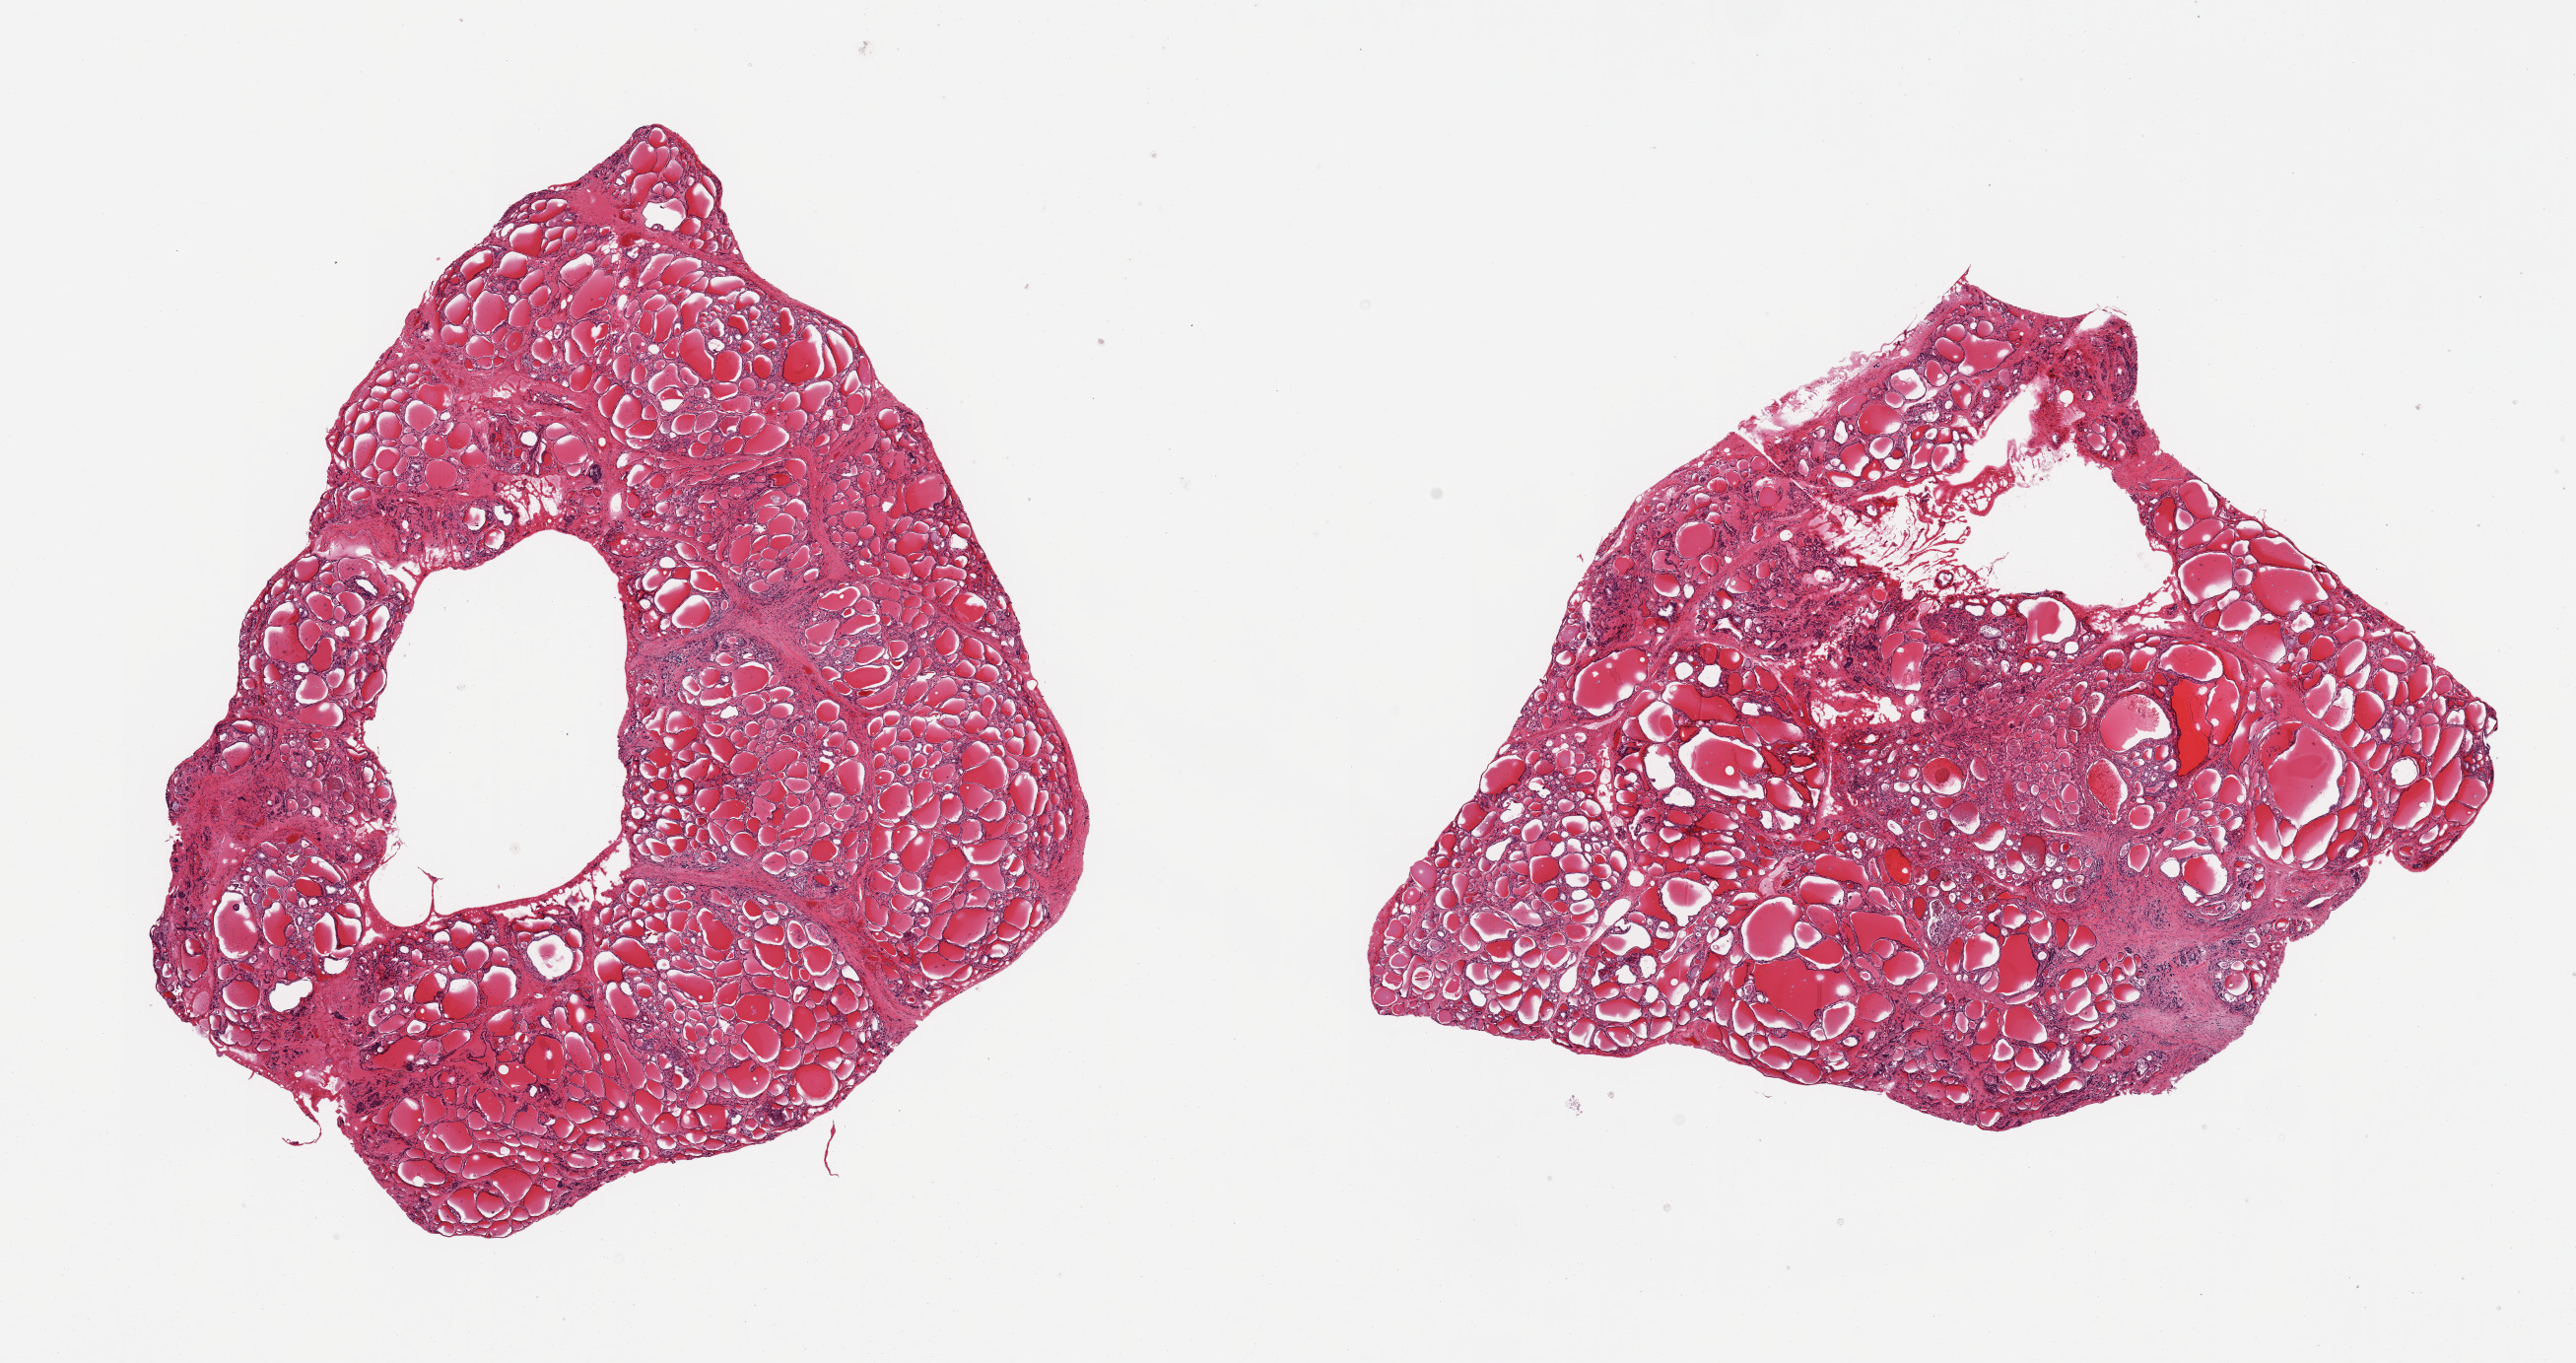
Whole-slide image, H&E stain, a low-resolution overview of the entire scanned area, about 20.7 x 10.9 mm (slide scanned at 20x); PAXgene-fixed paraffin-embedded (PFPE) section; sampled site (target tissue): thyroid; tissue donor sample.
* review note (as recorded): 2 pieces; foci of fibrosis and cysts